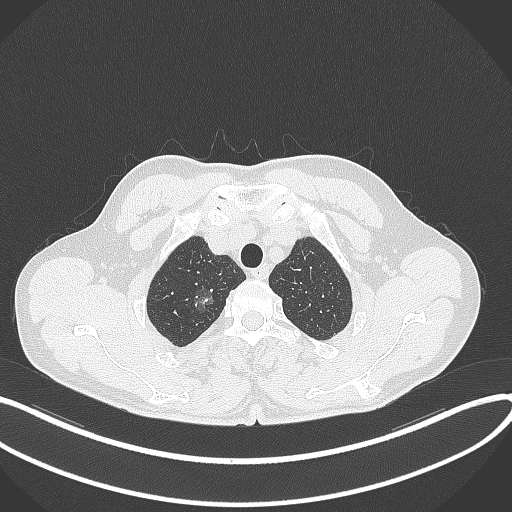
Chest CT, one axial slice; position 333 of 407 along the scan axis; reconstruction kernel B70f; lung window (W 1500 / L -600 HU); 1 mm slice thickness; 512 × 512 image matrix, field of view 400 × 400 mm. Patient: male, 58 years. From the clinical record (not read from this slice): clinical TNM (as recorded): T1c N0 M0; histopathological grade: G1-2.
Structures marked on this image (rectangle marked by the reading radiologist):
- lung tumour (recorded histology: adenocarcinoma): bounding box <190,282,220,318> (left, top, right, bottom; pixels)